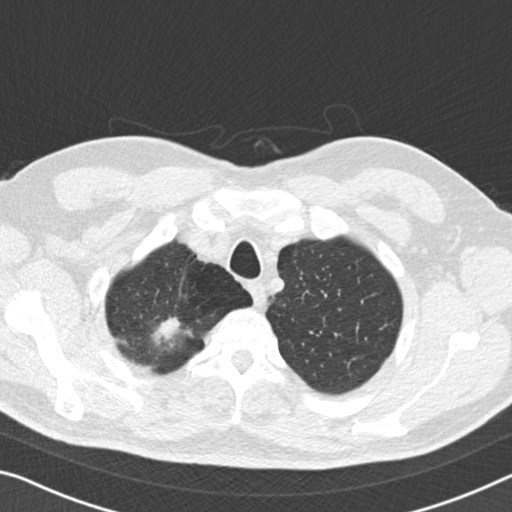
Low-dose screening chest CT, one axial slice; slice 145 of 167 in the series (ordered by position); reconstruction kernel B30f; 120 kVp; lung window (W 1500 / L -600 HU); 2 mm slice thickness; 512 × 512 image matrix, field of view 336 × 336 mm.
Outlined on this slice (expert manual segmentation):
- lesion 1 (tumor, upper lobe of right lung): bounding box (x1, y1, x2, y2) in pixels: (150, 318, 181, 344)